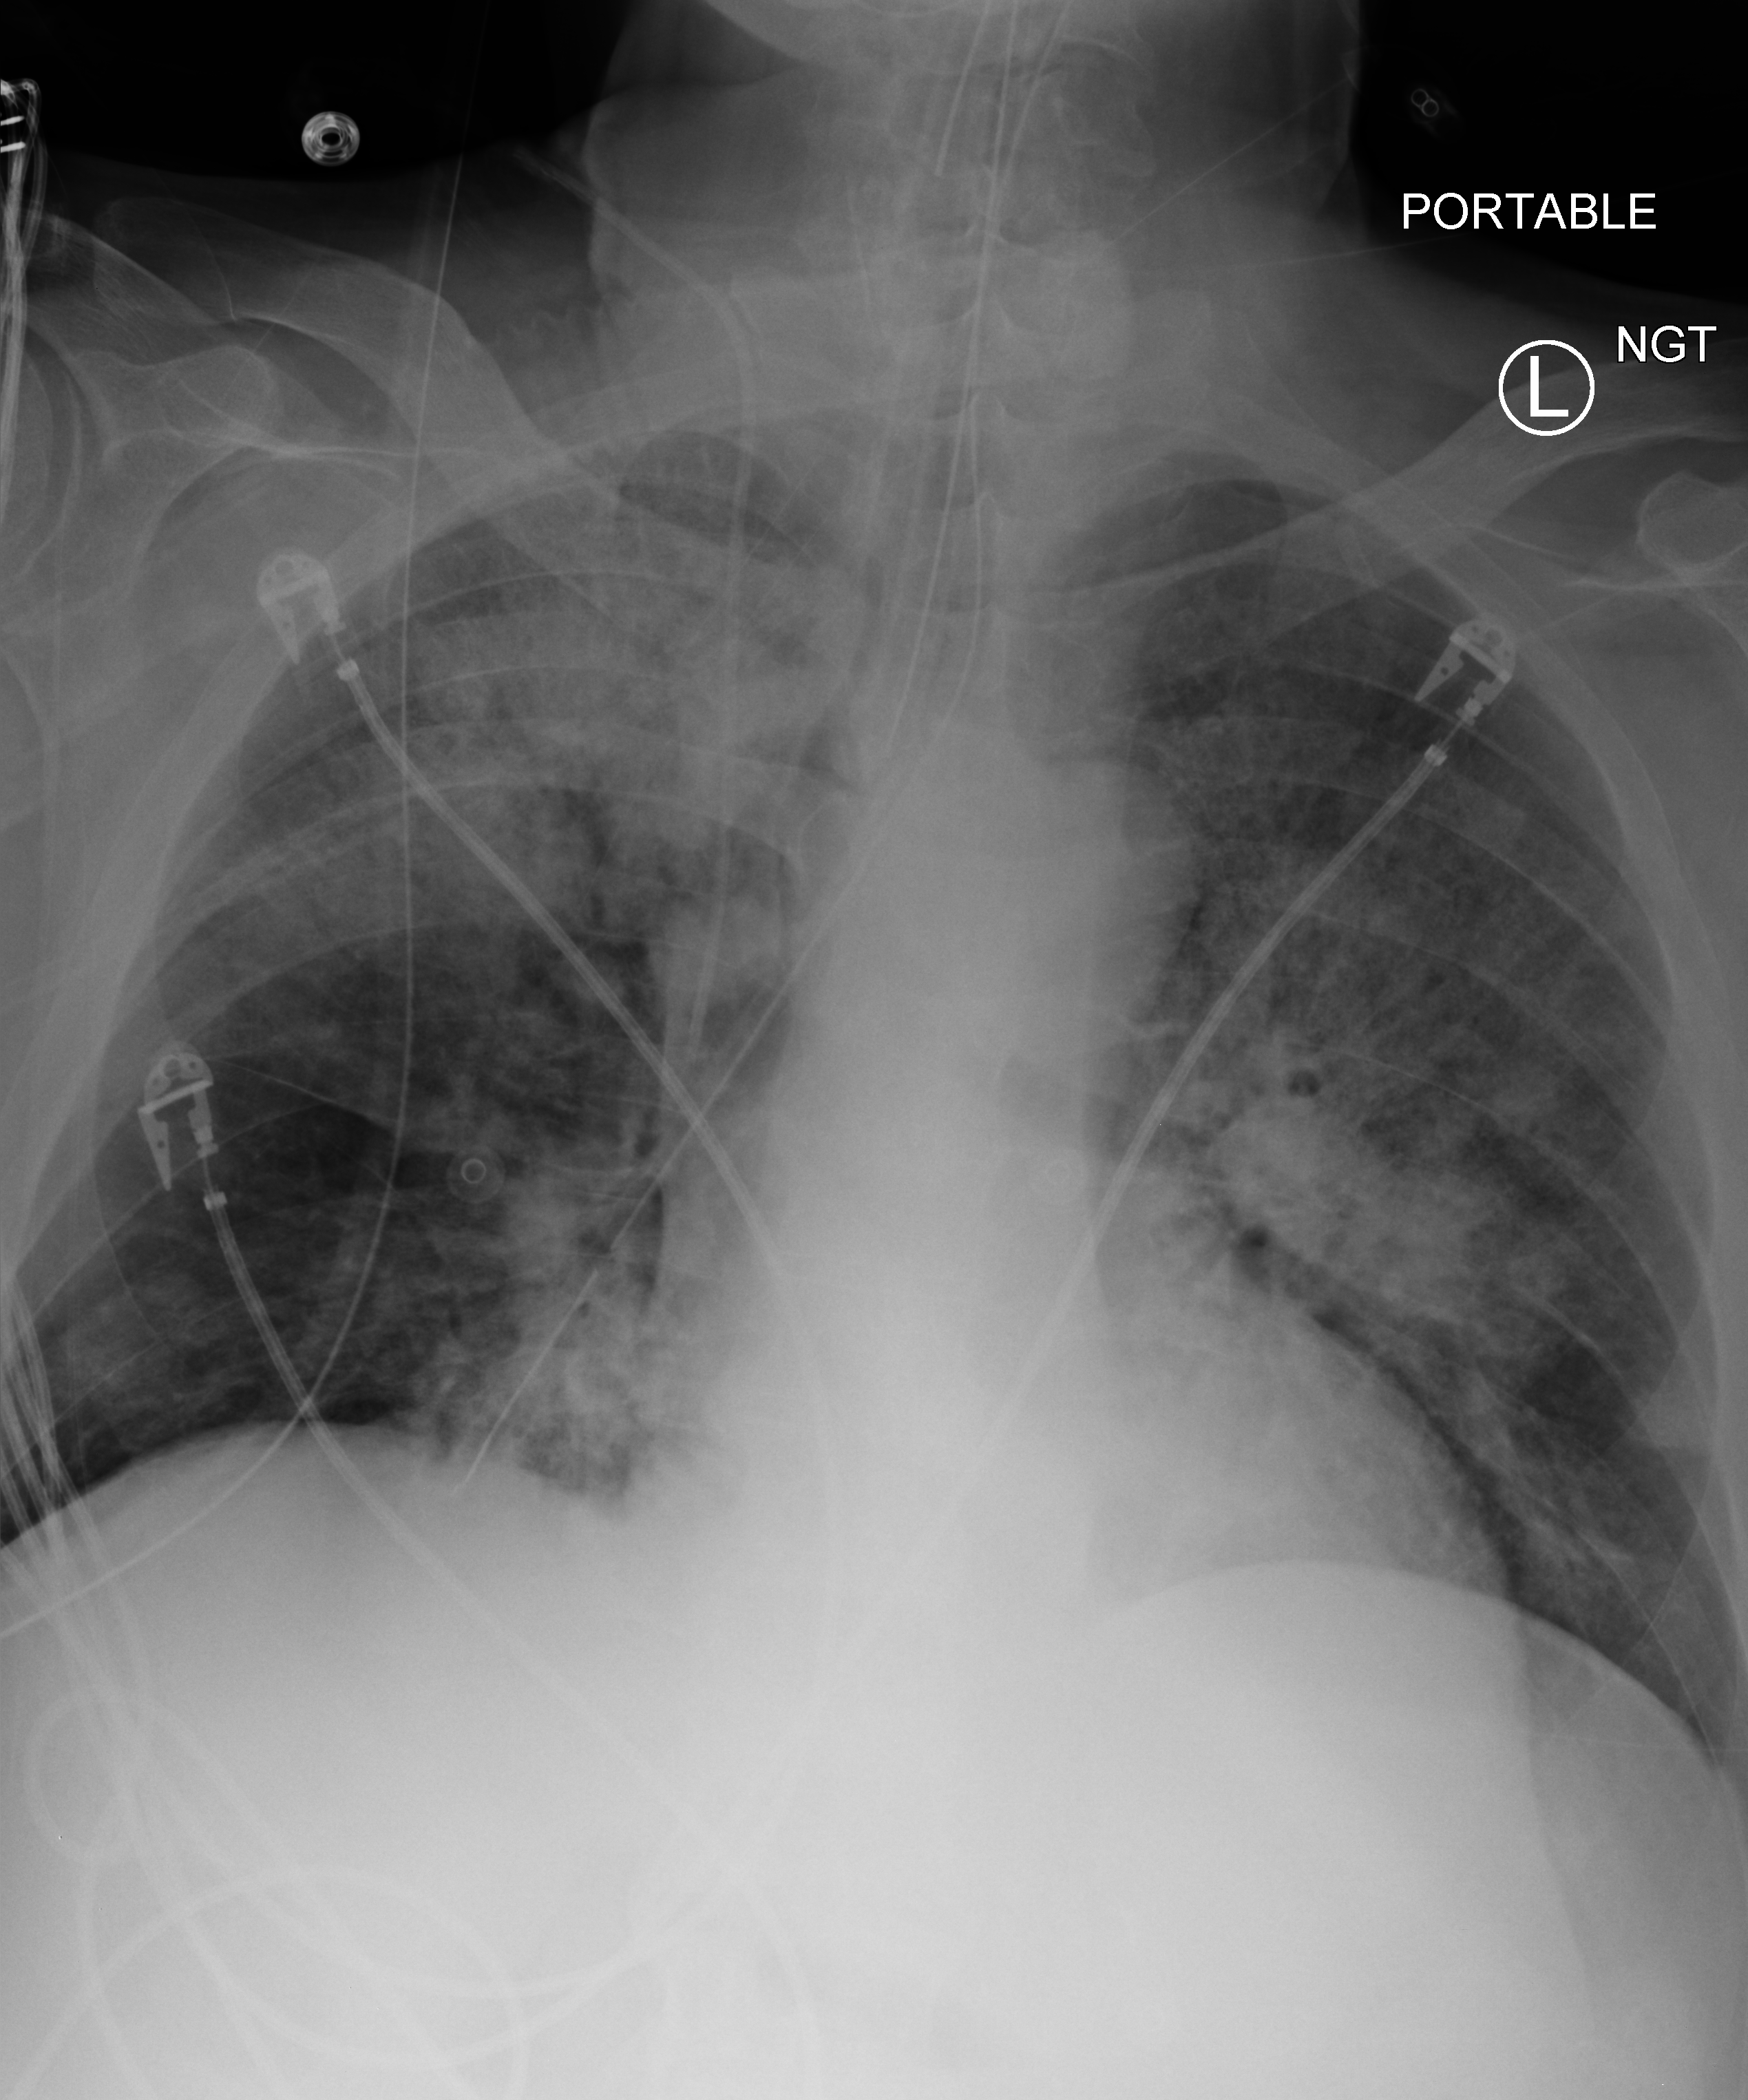
Chest X-ray (portable); anteroposterior (AP) projection. Male patient hospitalised with COVID-19, age 75–90 years.
Admission-level facts for this patient (not findings on this image; timing relative to this image not recorded): mechanically ventilated during this hospital stay: yes; admitted to intensive care during this hospital stay: yes; length of hospital stay: 2 days.